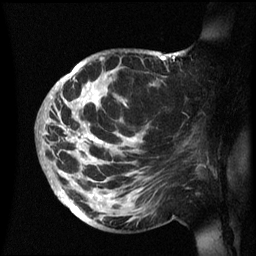
Breast MRI (dynamic contrast-enhanced), one sagittal slice. Position 37 of 60 along the scan axis. Dynamic contrast-enhanced series, image 2 of 3 at this slice position (ordered by acquisition). 1.5 T. TE 4.2 ms, TR 8.4 ms. 2.4 mm slice thickness. 256 × 256 image matrix. Patient: female, 48 years.
Annotated regions visible in this slice (semi-automatically segmented with operator editing):
- analysis volume of interest (the breast-tissue region the enhancement analysis was run in; not a lesion): bounding box <42,51,186,231> (left, top, right, bottom; pixels)
- tumour enhancement mask (voxels above the 70 % enhancement threshold inside the analysis volume of interest): <42,53,179,212>